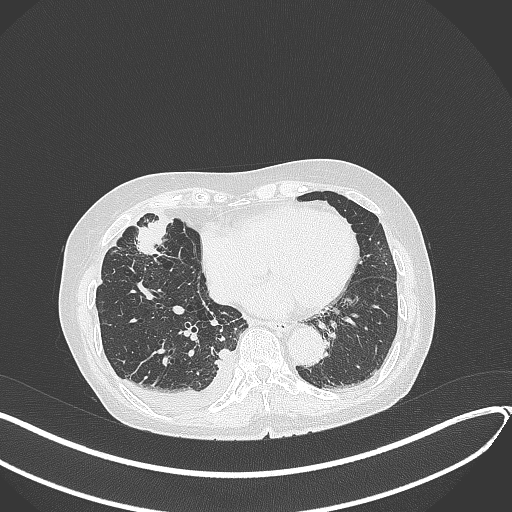
Chest CT, one axial slice. Slice 131 of 418 in the series (ordered by position). Reconstruction kernel B70f. Lung window (W 1500 / L -600 HU). 1 mm slice thickness. 512 × 512 image matrix. Female patient, age 75 years. From the clinical record (not read from this slice): clinical TNM (as recorded): T2a N3 M0.
Structures marked on this image (bounding box drawn by a radiologist):
- lung tumour (recorded histology: adenocarcinoma): bounding box [x1, y1, x2, y2] px = [136, 214, 167, 261]